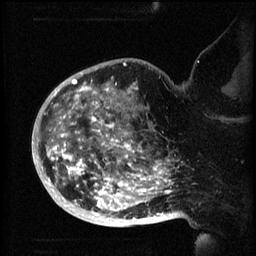
Breast MRI (dynamic contrast-enhanced), one sagittal slice; slice 44 of 60 in the series (ordered by position); 3 images stored at this slice position (order not interpretable as contrast timing); 1.5 T; TE 4.2 ms, TR 8.2 ms; 2 mm slice thickness; 256 × 256 image matrix, field of view 200 × 200 mm. Patient: female, 50 years.
Outlined on this slice (semi-automatic segmentation, software-assisted and operator-edited):
- analysis volume of interest (the breast-tissue region the enhancement analysis was run in; not a lesion): box from (x=44, y=72) to (x=173, y=219) px
- tumour enhancement mask (voxels above the 70 % enhancement threshold inside the analysis volume of interest): (x=47, y=72)–(x=173, y=219)